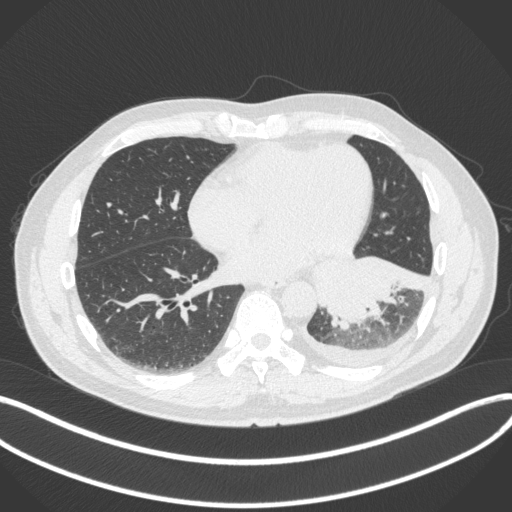
Chest CT, one axial slice; slice 137 of 350 in the series (ordered by position); 120 kVp; lung window (W 1500 / L -600 HU); 512 × 512 image matrix, field of view 400 × 400 mm. Patient: male, 58 years. From the clinical record (not read from this slice): clinical TNM (as recorded): T3 N1 M1b; histopathological grade: G3.
Annotated regions visible in this slice (bounding box drawn by a radiologist):
- lung tumour (recorded histology: small cell carcinoma): bounding box (x1, y1, x2, y2) in pixels: (316, 252, 433, 332)